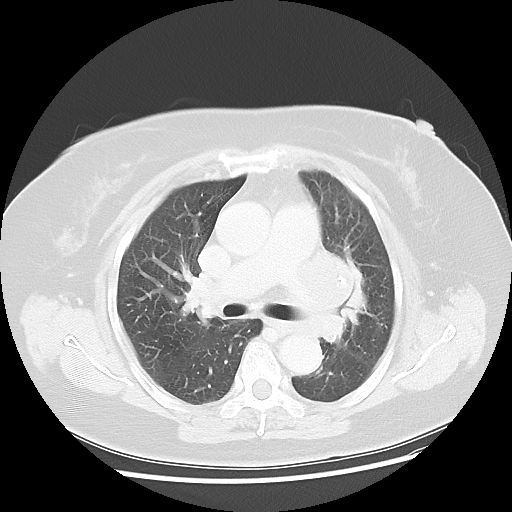
Chest CT, one axial slice; slice 28 of 49 in the series (ordered by position); reconstruction kernel LUNG; 120 kVp; lung window (W 1500 / L -600 HU); 512 × 512 image matrix, field of view 374 × 374 mm. Female patient, age 58 years. Case-level facts recorded for this patient, not image findings: clinical TNM (as recorded): T4 N3 M0.
Annotated regions visible in this slice (rectangle marked by the reading radiologist):
- lung tumour (recorded histology: small cell carcinoma): bounding box [x1, y1, x2, y2] px = [322, 243, 378, 356]